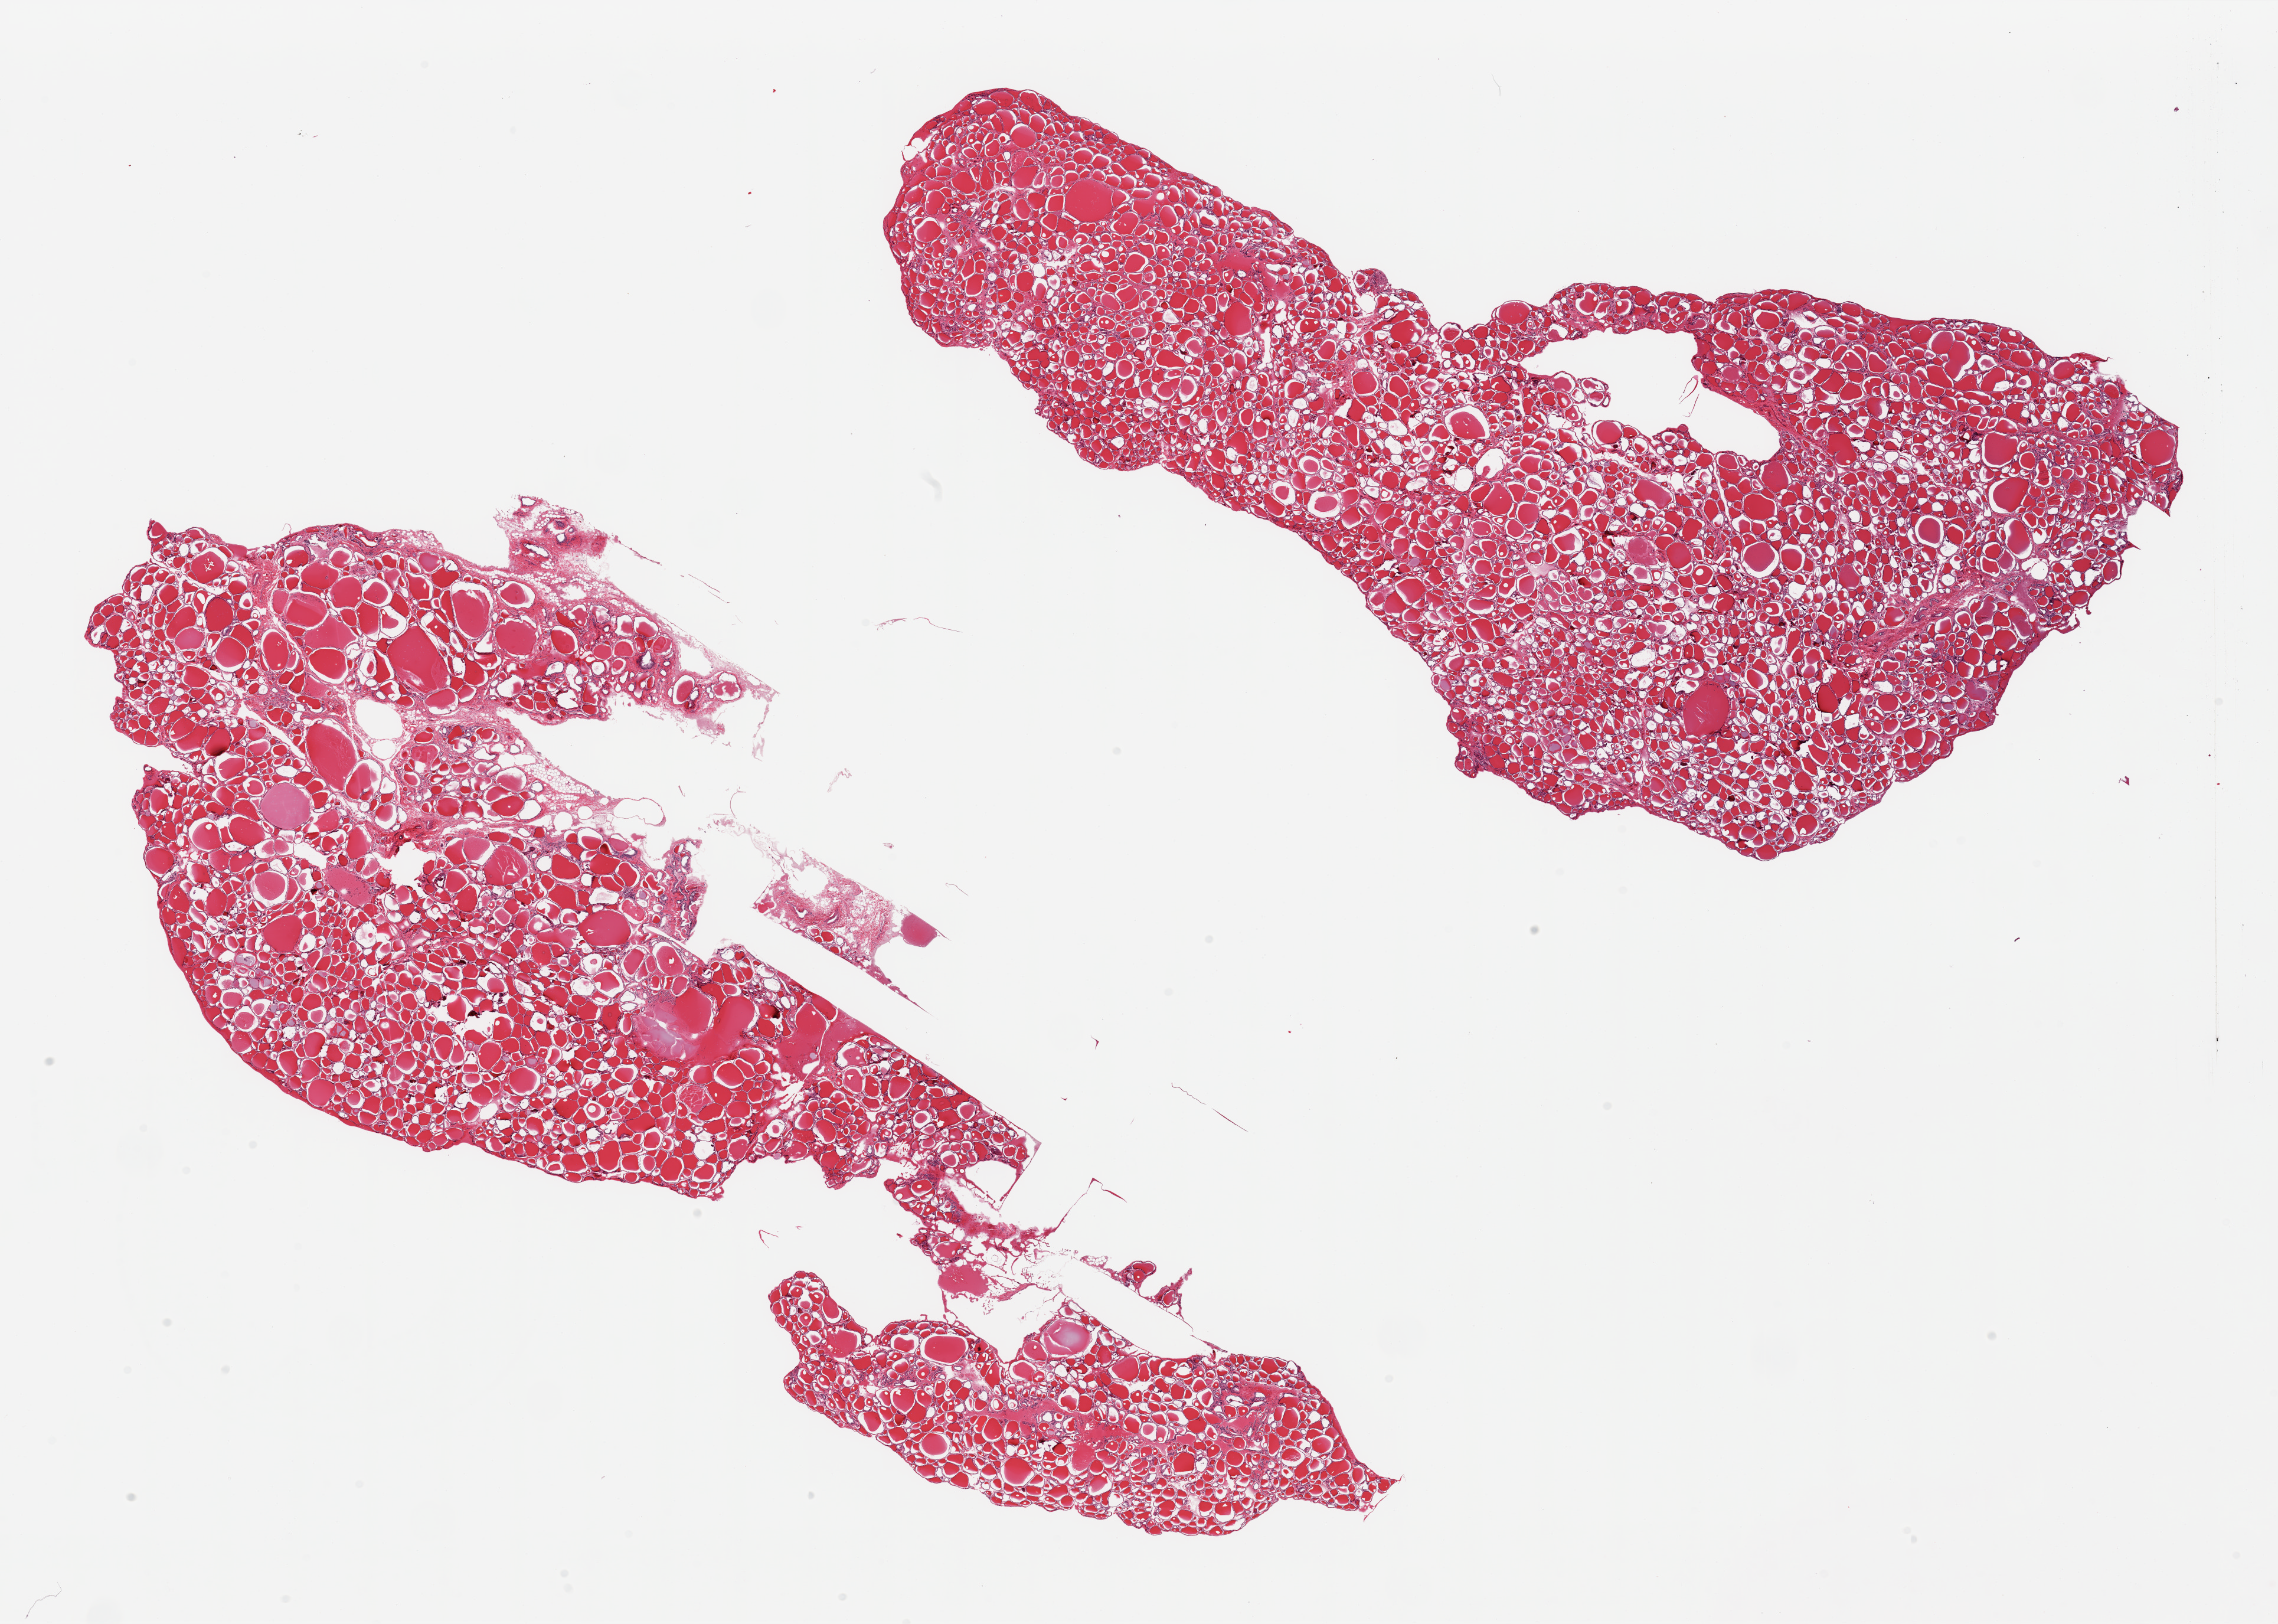
H&E whole-slide image — shown as a low-resolution overview of the whole scanned area (about 30.5 x 21.8 mm); PAXgene-fixed, paraffin-embedded tissue; section of thyroid (target tissue); donor tissue sample. Donor sex: female.
Reviewer comment on this tissue sample: 2 pieces, no significant abnormalities noted.